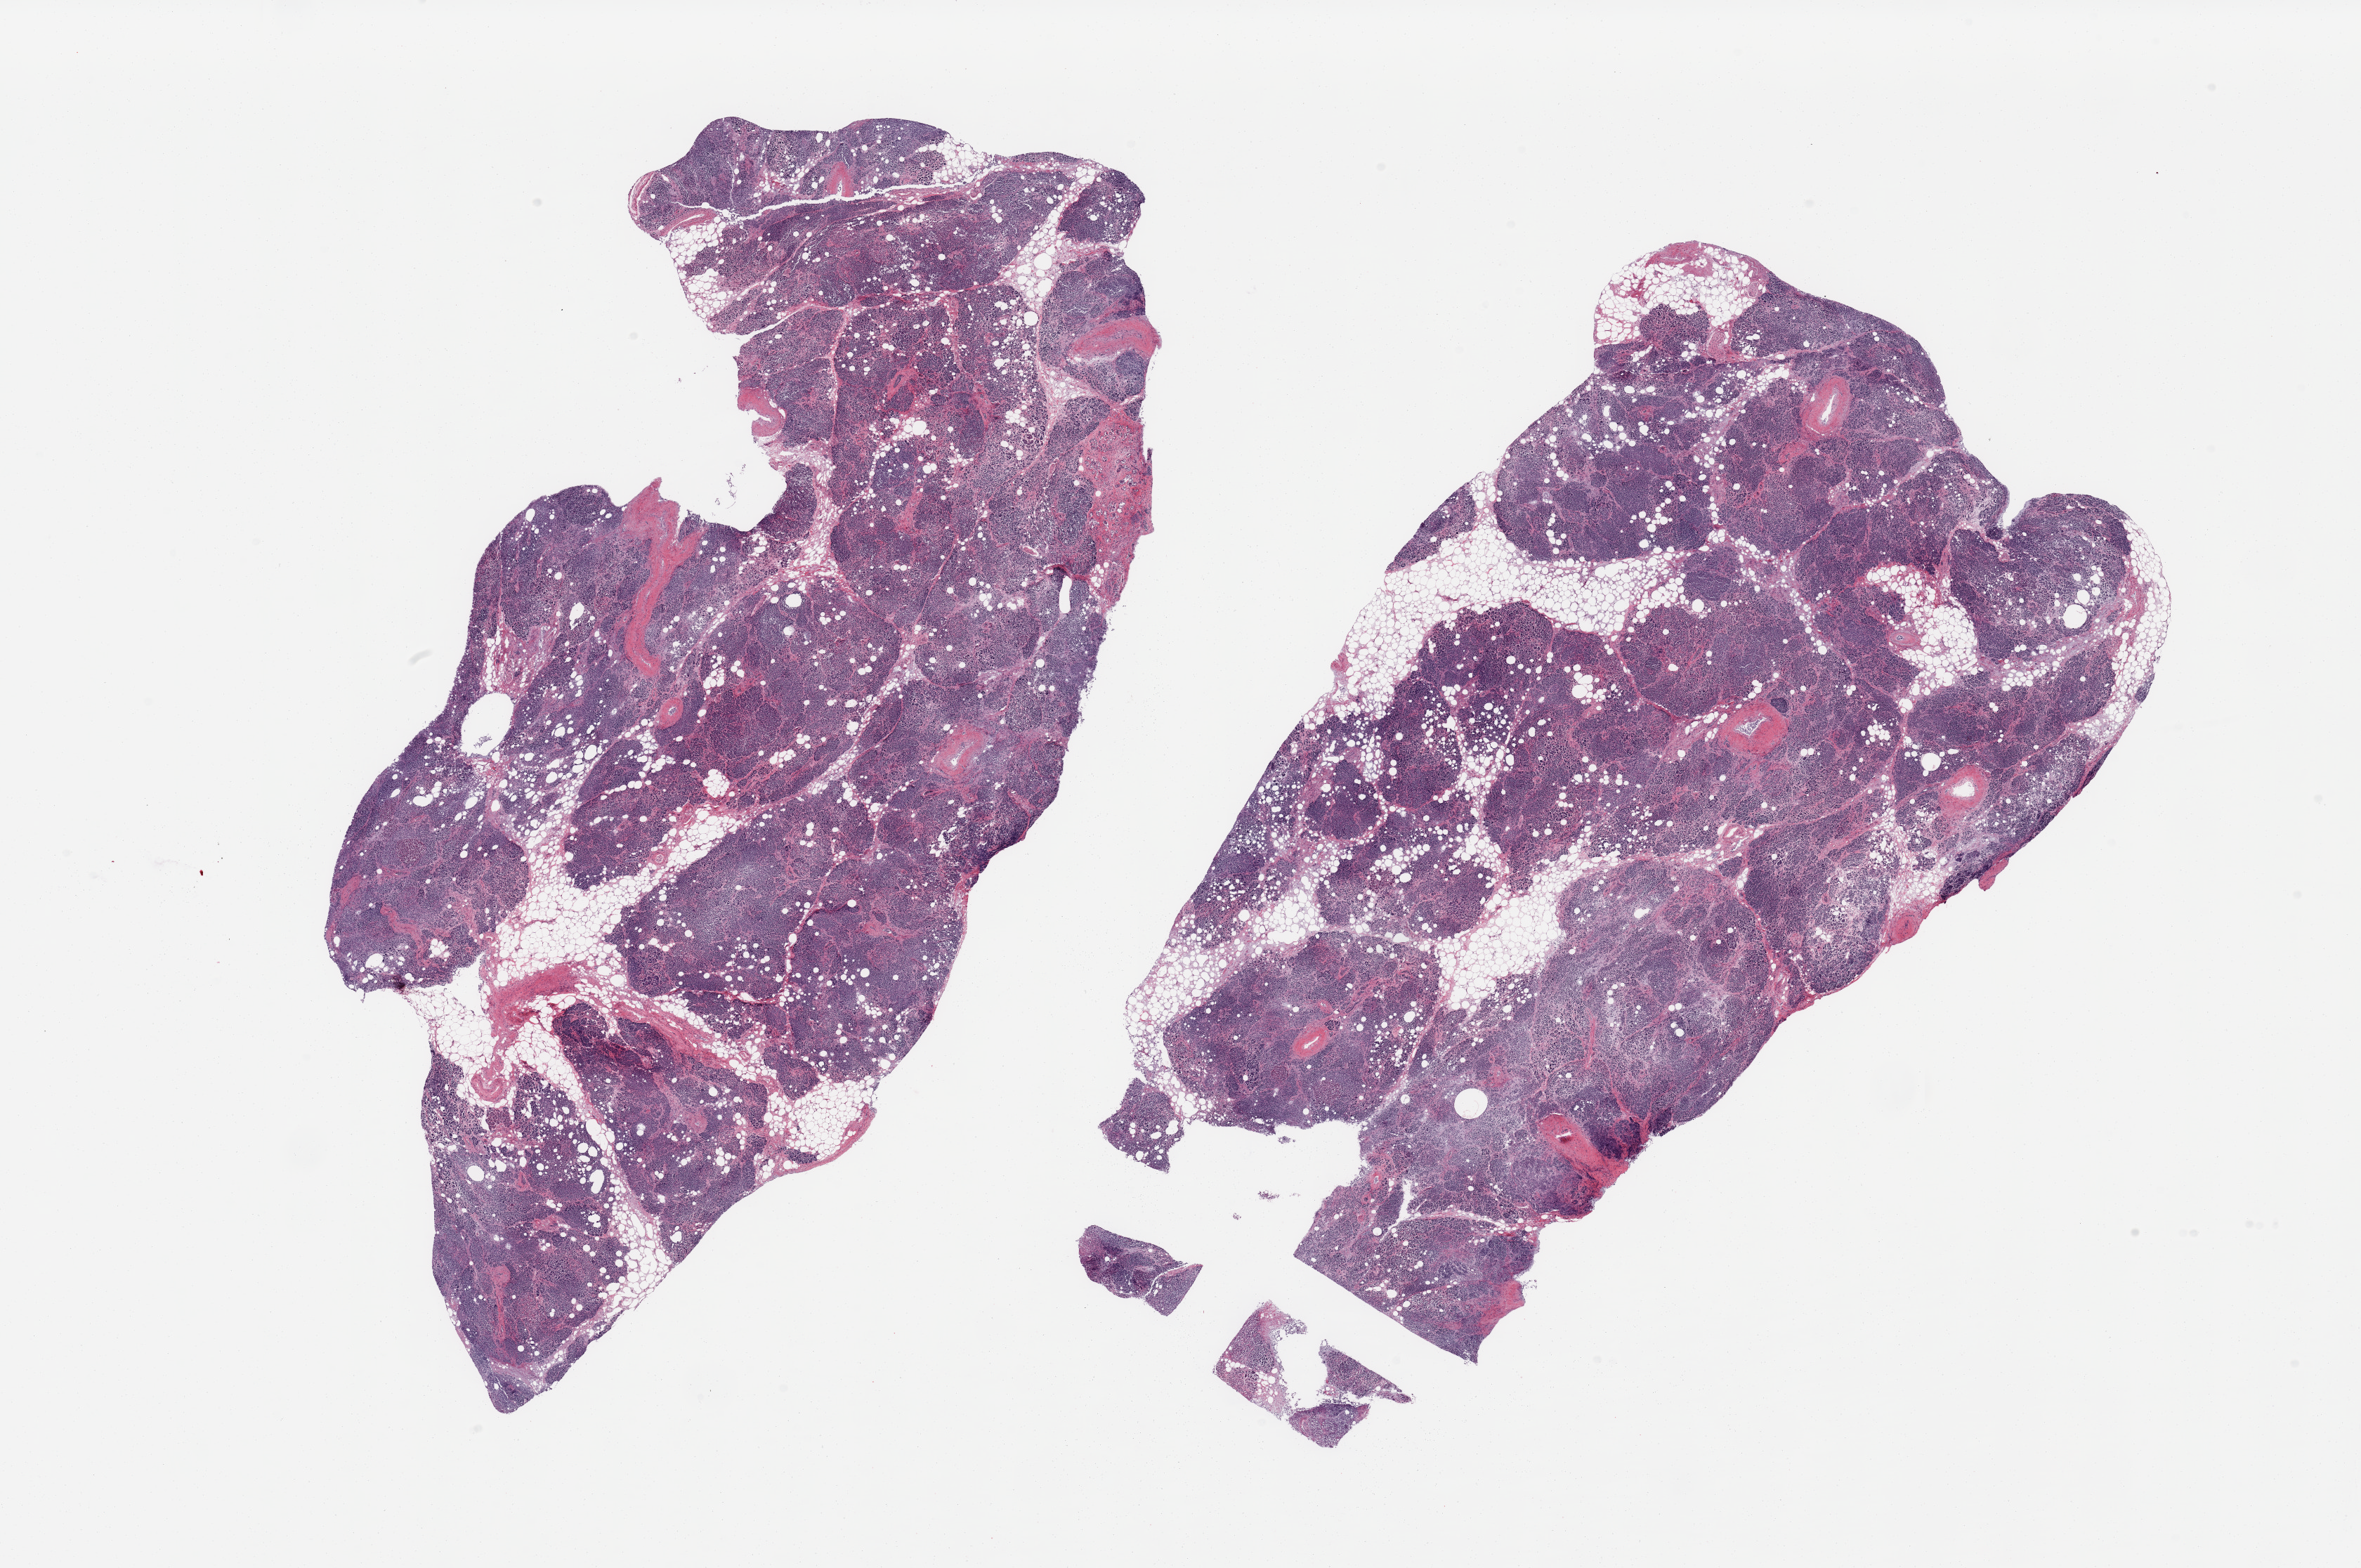
Whole-slide image, haematoxylin and eosin stain, low-resolution overview of the scanned area, about 26.6 x 17.7 mm (acquisition: 20x scan). PAXgene-fixed, paraffin-embedded tissue. Section of pancreas (target tissue). Tissue donor sample. Donor: male.
Reviewer comment on this tissue sample: 2 pieces; ~20% internal fat; parenchymal and fat tissue moderate to severe autolysis; focal interstitial fibrosis and parenchymal atrophy.